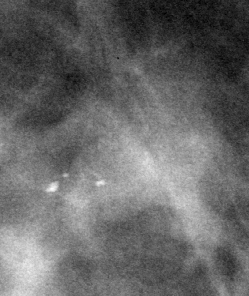
Crop from a digitized film mammogram around one marked abnormality, left breast, CC view, BI-RADS breast density category 2 (scale 1–4).
- Finding: calcifications, morphology punctate, distribution clustered; BI-RADS assessment category 4; pathology result (as recorded, not read from the image): benign.